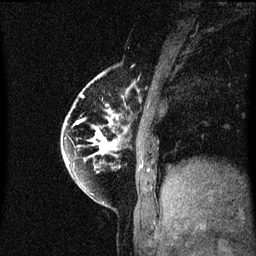
Breast MRI (dynamic contrast-enhanced), one sagittal slice; position 14 of 60 along the scan axis; dynamic contrast-enhanced series, image 2 of 3 at this slice position (ordered by acquisition); 1.5 T; TE 4.2 ms, TR 8.4 ms; 256 × 256 image matrix, field of view 200 × 200 mm. Female patient, age 60 years.
Annotated regions visible in this slice (semi-automatically segmented with operator editing):
- analysis volume of interest (the breast-tissue region the enhancement analysis was run in; not a lesion): bounding box <64,70,127,195> (left, top, right, bottom; pixels)
- tumour enhancement mask (voxels above the 70 % enhancement threshold inside the analysis volume of interest): <64,74,127,167>